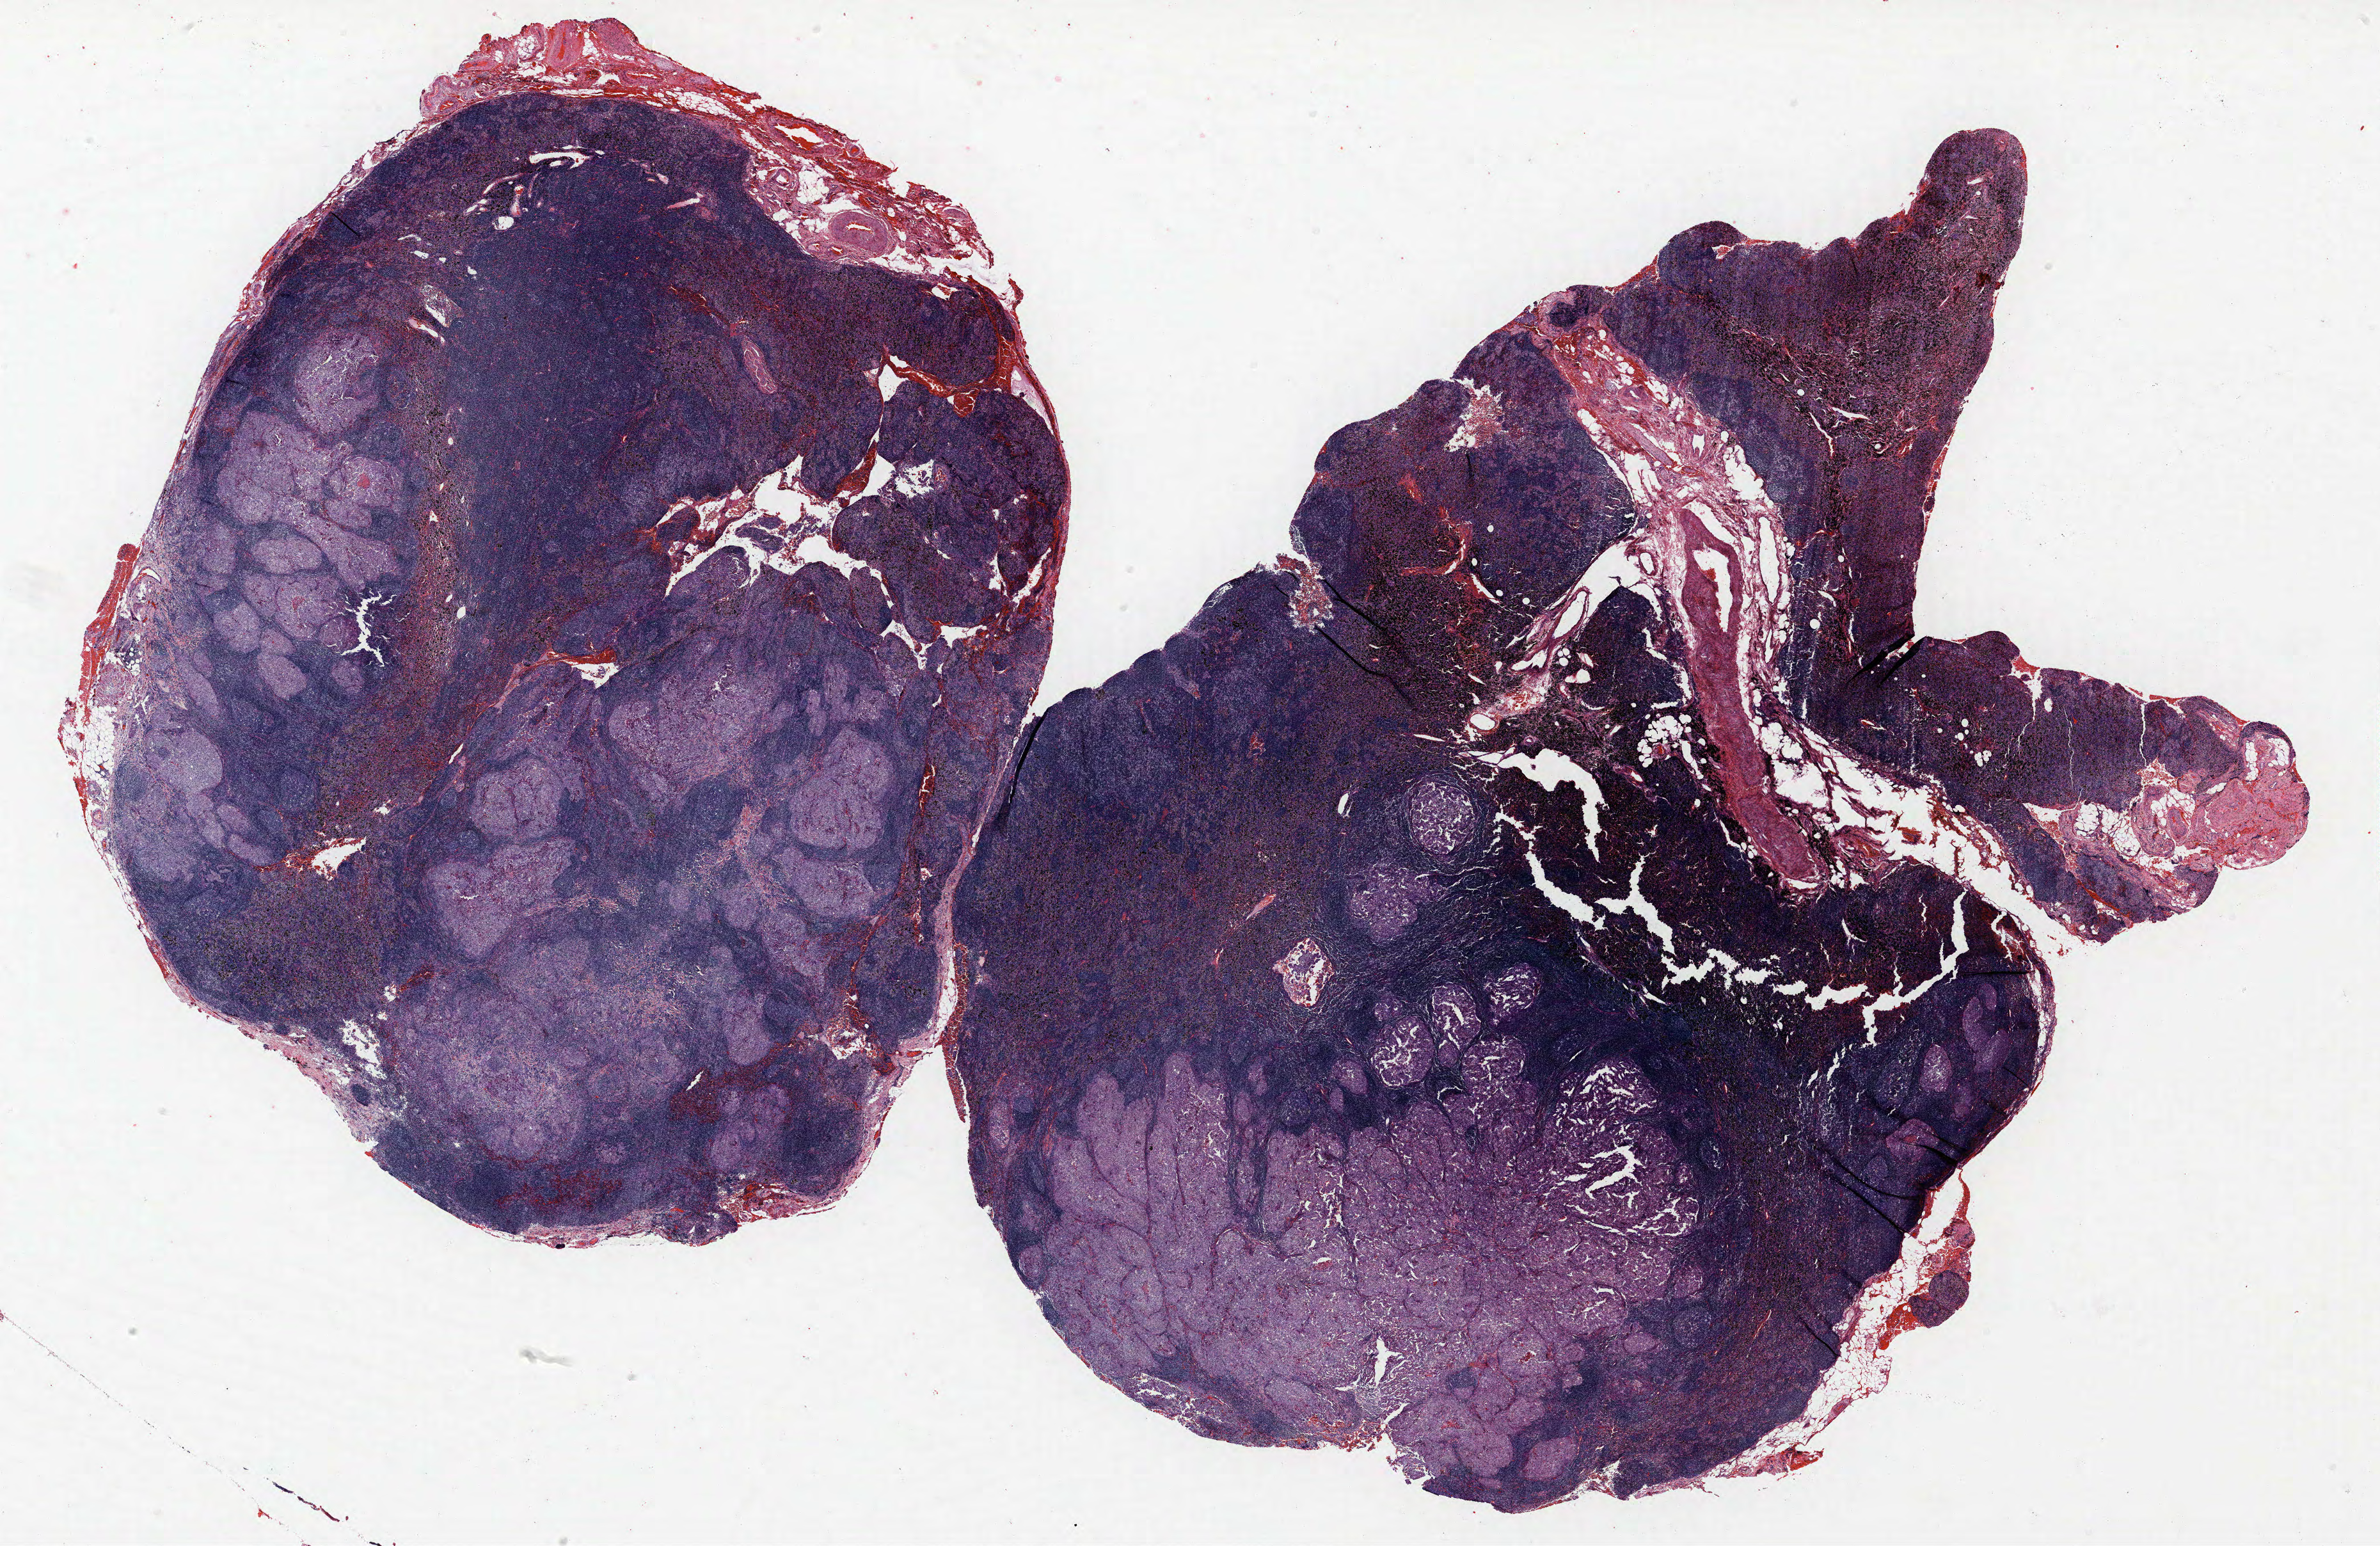
H&E whole-slide image, whole scanned area (about 29.8 x 19.3 mm, from a 40x scan) shown as a low-resolution overview. FFPE section. Lung tissue. Male patient, aged 72 at enrolment. Former smoker at enrolment. Grade: moderately differentiated (G2).
* primary tumour location (clinical record): right upper lobe
* tumour size (pathology): 12 mm
* stage (AJCC 6th edition): IIA
* participant's lung-cancer diagnosis: Adenocarcinoma, NOS (ICD-O-3 8140/3)